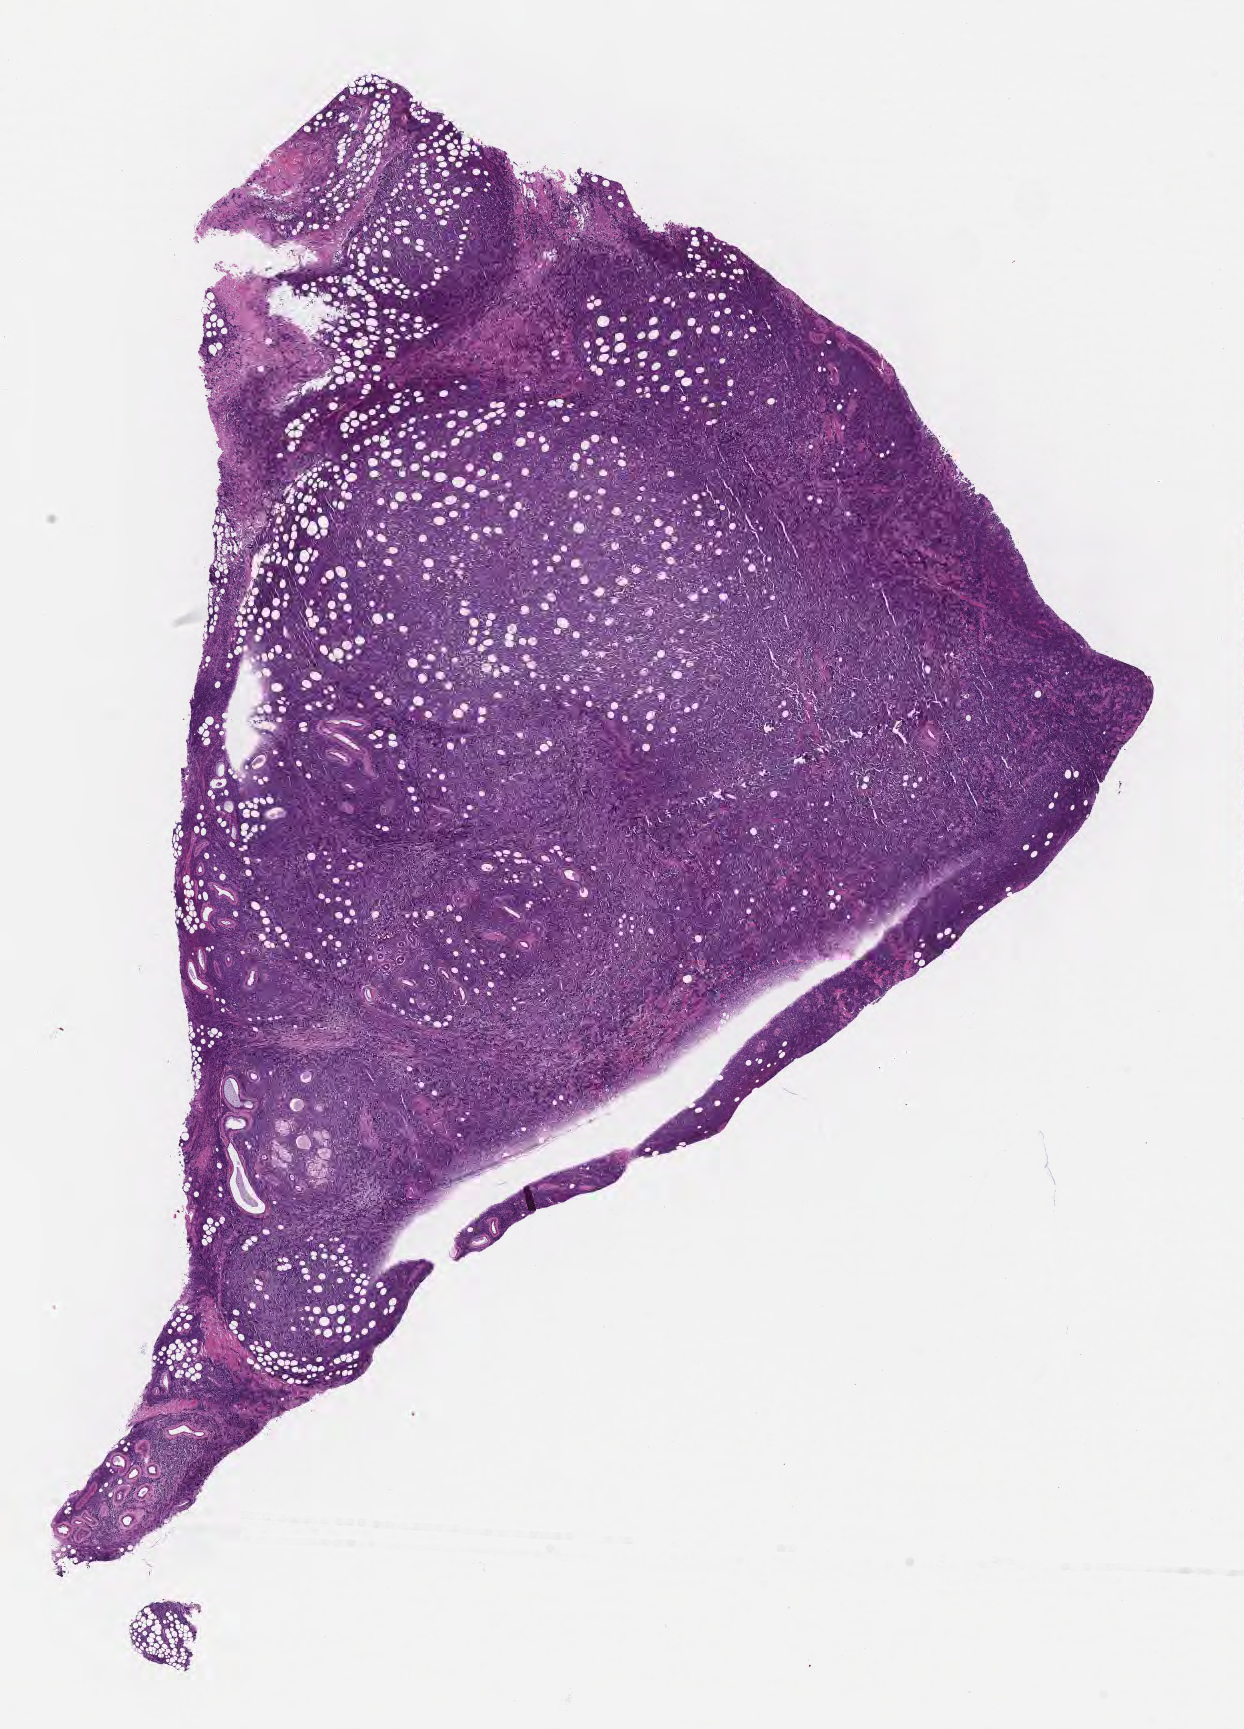
Digitized haematoxylin and eosin-stained section — whole scanned area (about 10.1 x 14.0 mm) shown as a low-resolution overview. FFPE section. Specimen: primary tumor. Patient: male, 46 years old. Slide review estimates, as recorded: tumor cells 85%, tumor nuclei 95%, stromal cells 10%, necrosis 5%, normal cells 0%. Infiltration values recorded for this section: lymphocyte infiltration 50%, monocyte infiltration 25%, neutrophil infiltration 5%.
• Ann Arbor stage (patient): Stage IV
• section: top of the tissue portion
• diagnosis: Burkitt lymphoma, NOS